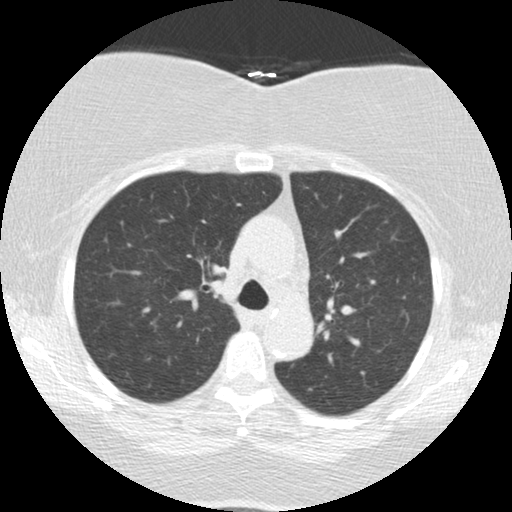
Low-dose screening chest CT, one axial slice; position 95 of 136 along the scan axis; reconstruction kernel STANDARD; lung window (W 1500 / L -600 HU); 2.5 mm slice thickness; 512 × 512 image matrix, field of view 309 × 309 mm.
Annotated regions visible in this slice (outlined manually by an expert reader):
- lesion 1 (tumor): box from (x=210, y=280) to (x=224, y=295) px